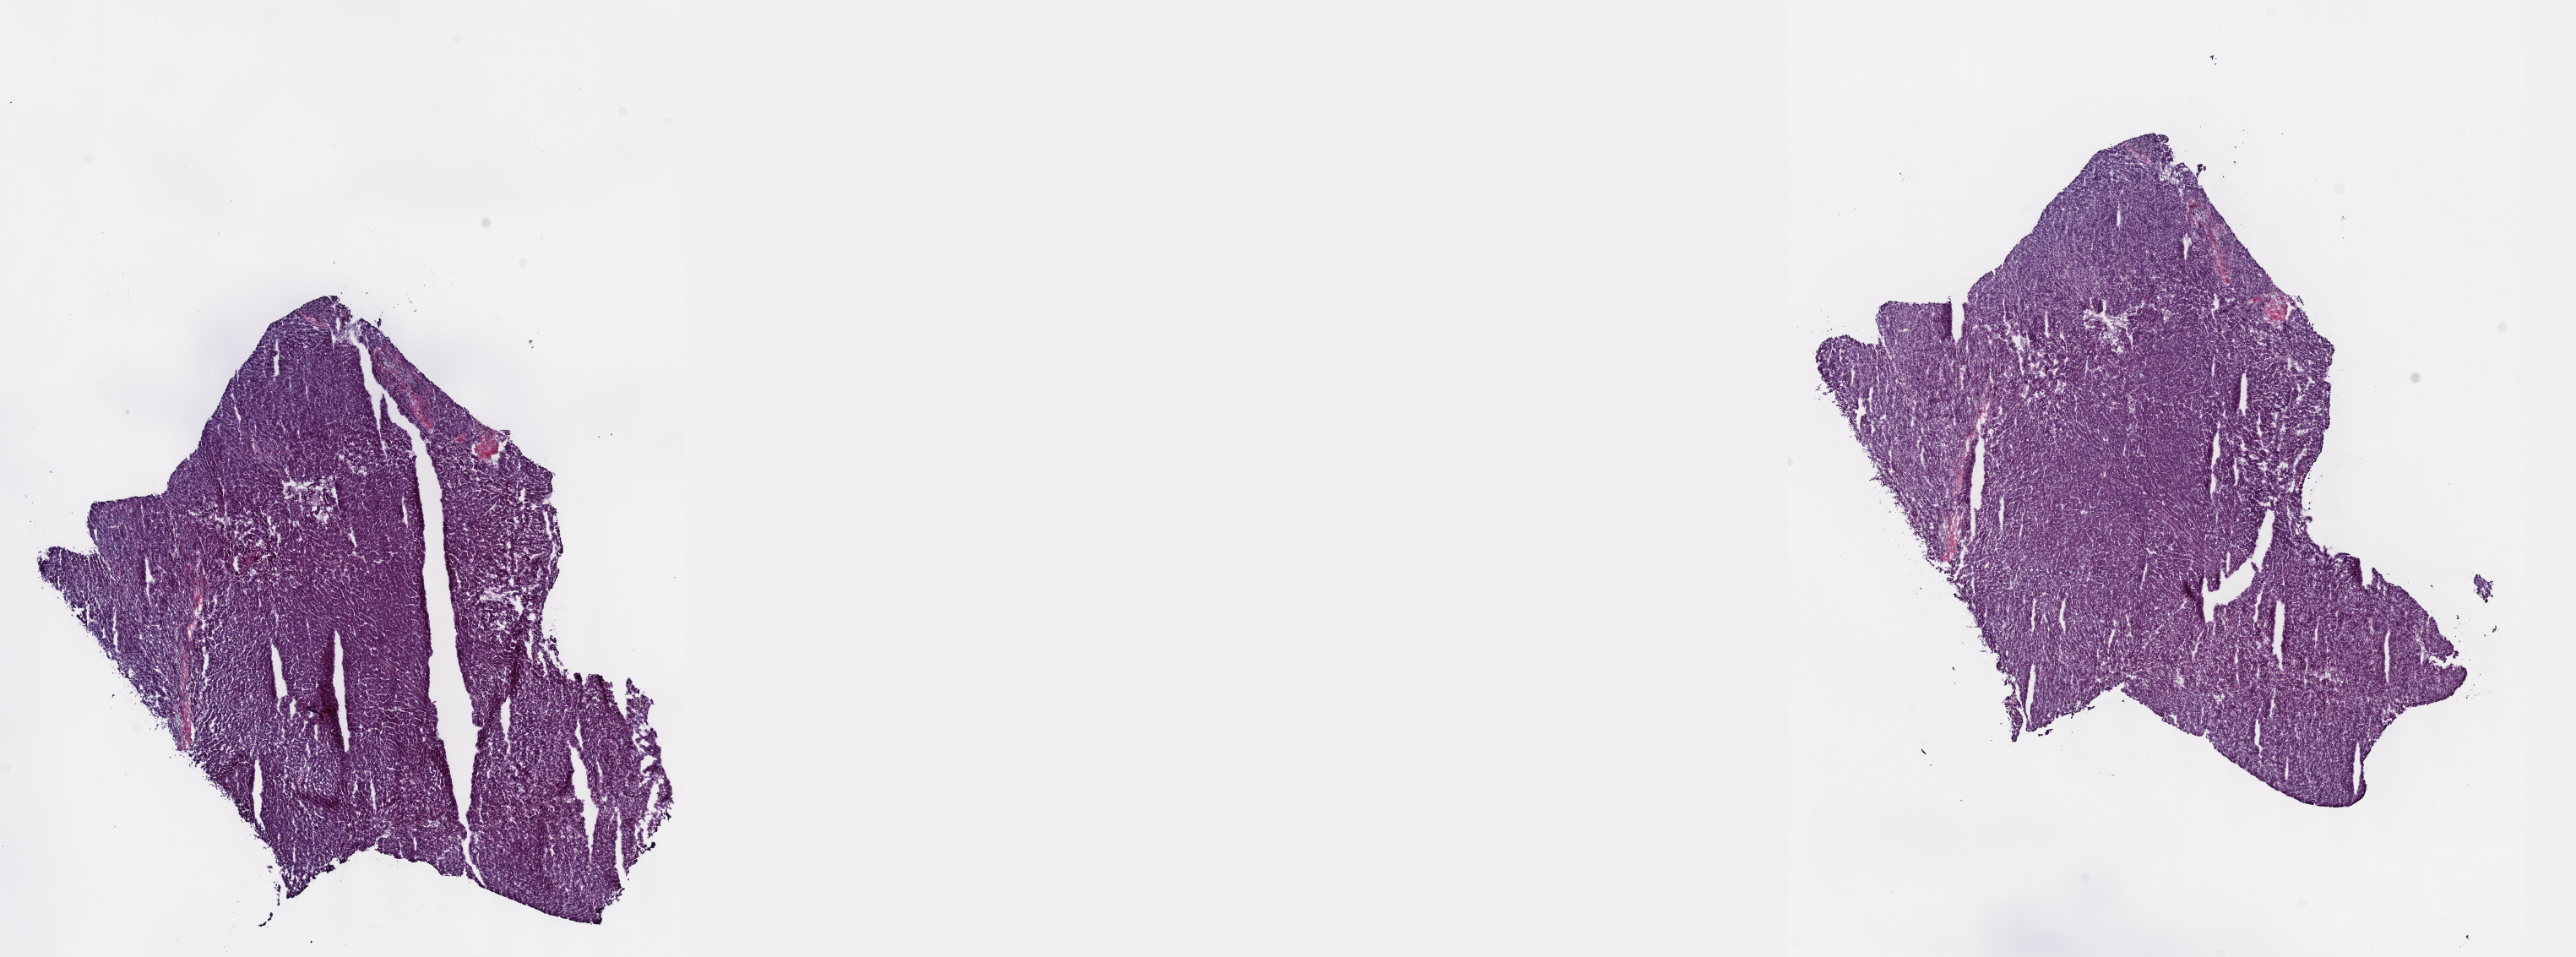
Digitized H&E-stained tissue section (whole slide) — shown as a low-resolution overview of the whole scanned area (about 24.6 x 9.2 mm). Frozen section from the top of the tissue portion. Liver, primary tumour sample. Female, age 81 years at initial diagnosis. Histologic grade: G2 (moderately differentiated). Composition of this section per pathologist review: tumour cells 85%, tumour nuclei 85%, normal cells 0%, stromal cells 15%, necrosis 0%. Inflammatory infiltration, as recorded: lymphocyte infiltration 3%, monocyte infiltration 1%, neutrophil infiltration 2%.
* AJCC pathologic stage: I (7th edition)
* histologic diagnosis: Hepatocellular carcinoma, NOS